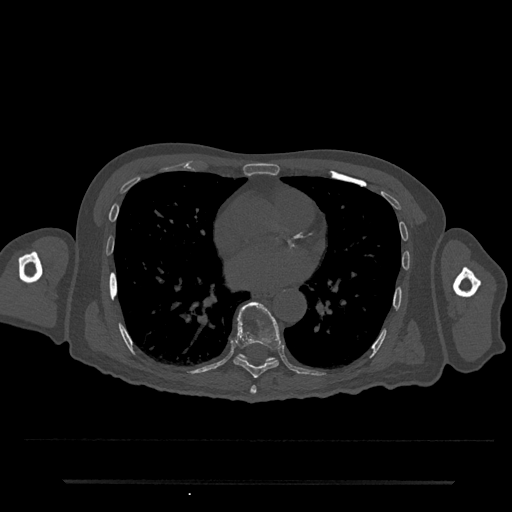
CT including the spine, one axial slice; slice 412 of 797 in the series (ordered by position); 120 kVp; bone window (W 1800 / L 400 HU); 512 × 512 image matrix. Male patient, age 74 years. From the clinical record (not read from this slice): primary cancer: prostate.
Annotated regions visible in this slice (semi-automatically segmented with operator editing):
- T7 vertebra: bounding box [x1, y1, x2, y2] px = [250, 386, 257, 394]
- T8 vertebra: [233, 302, 281, 379]
- T9 vertebra: [239, 353, 275, 362]